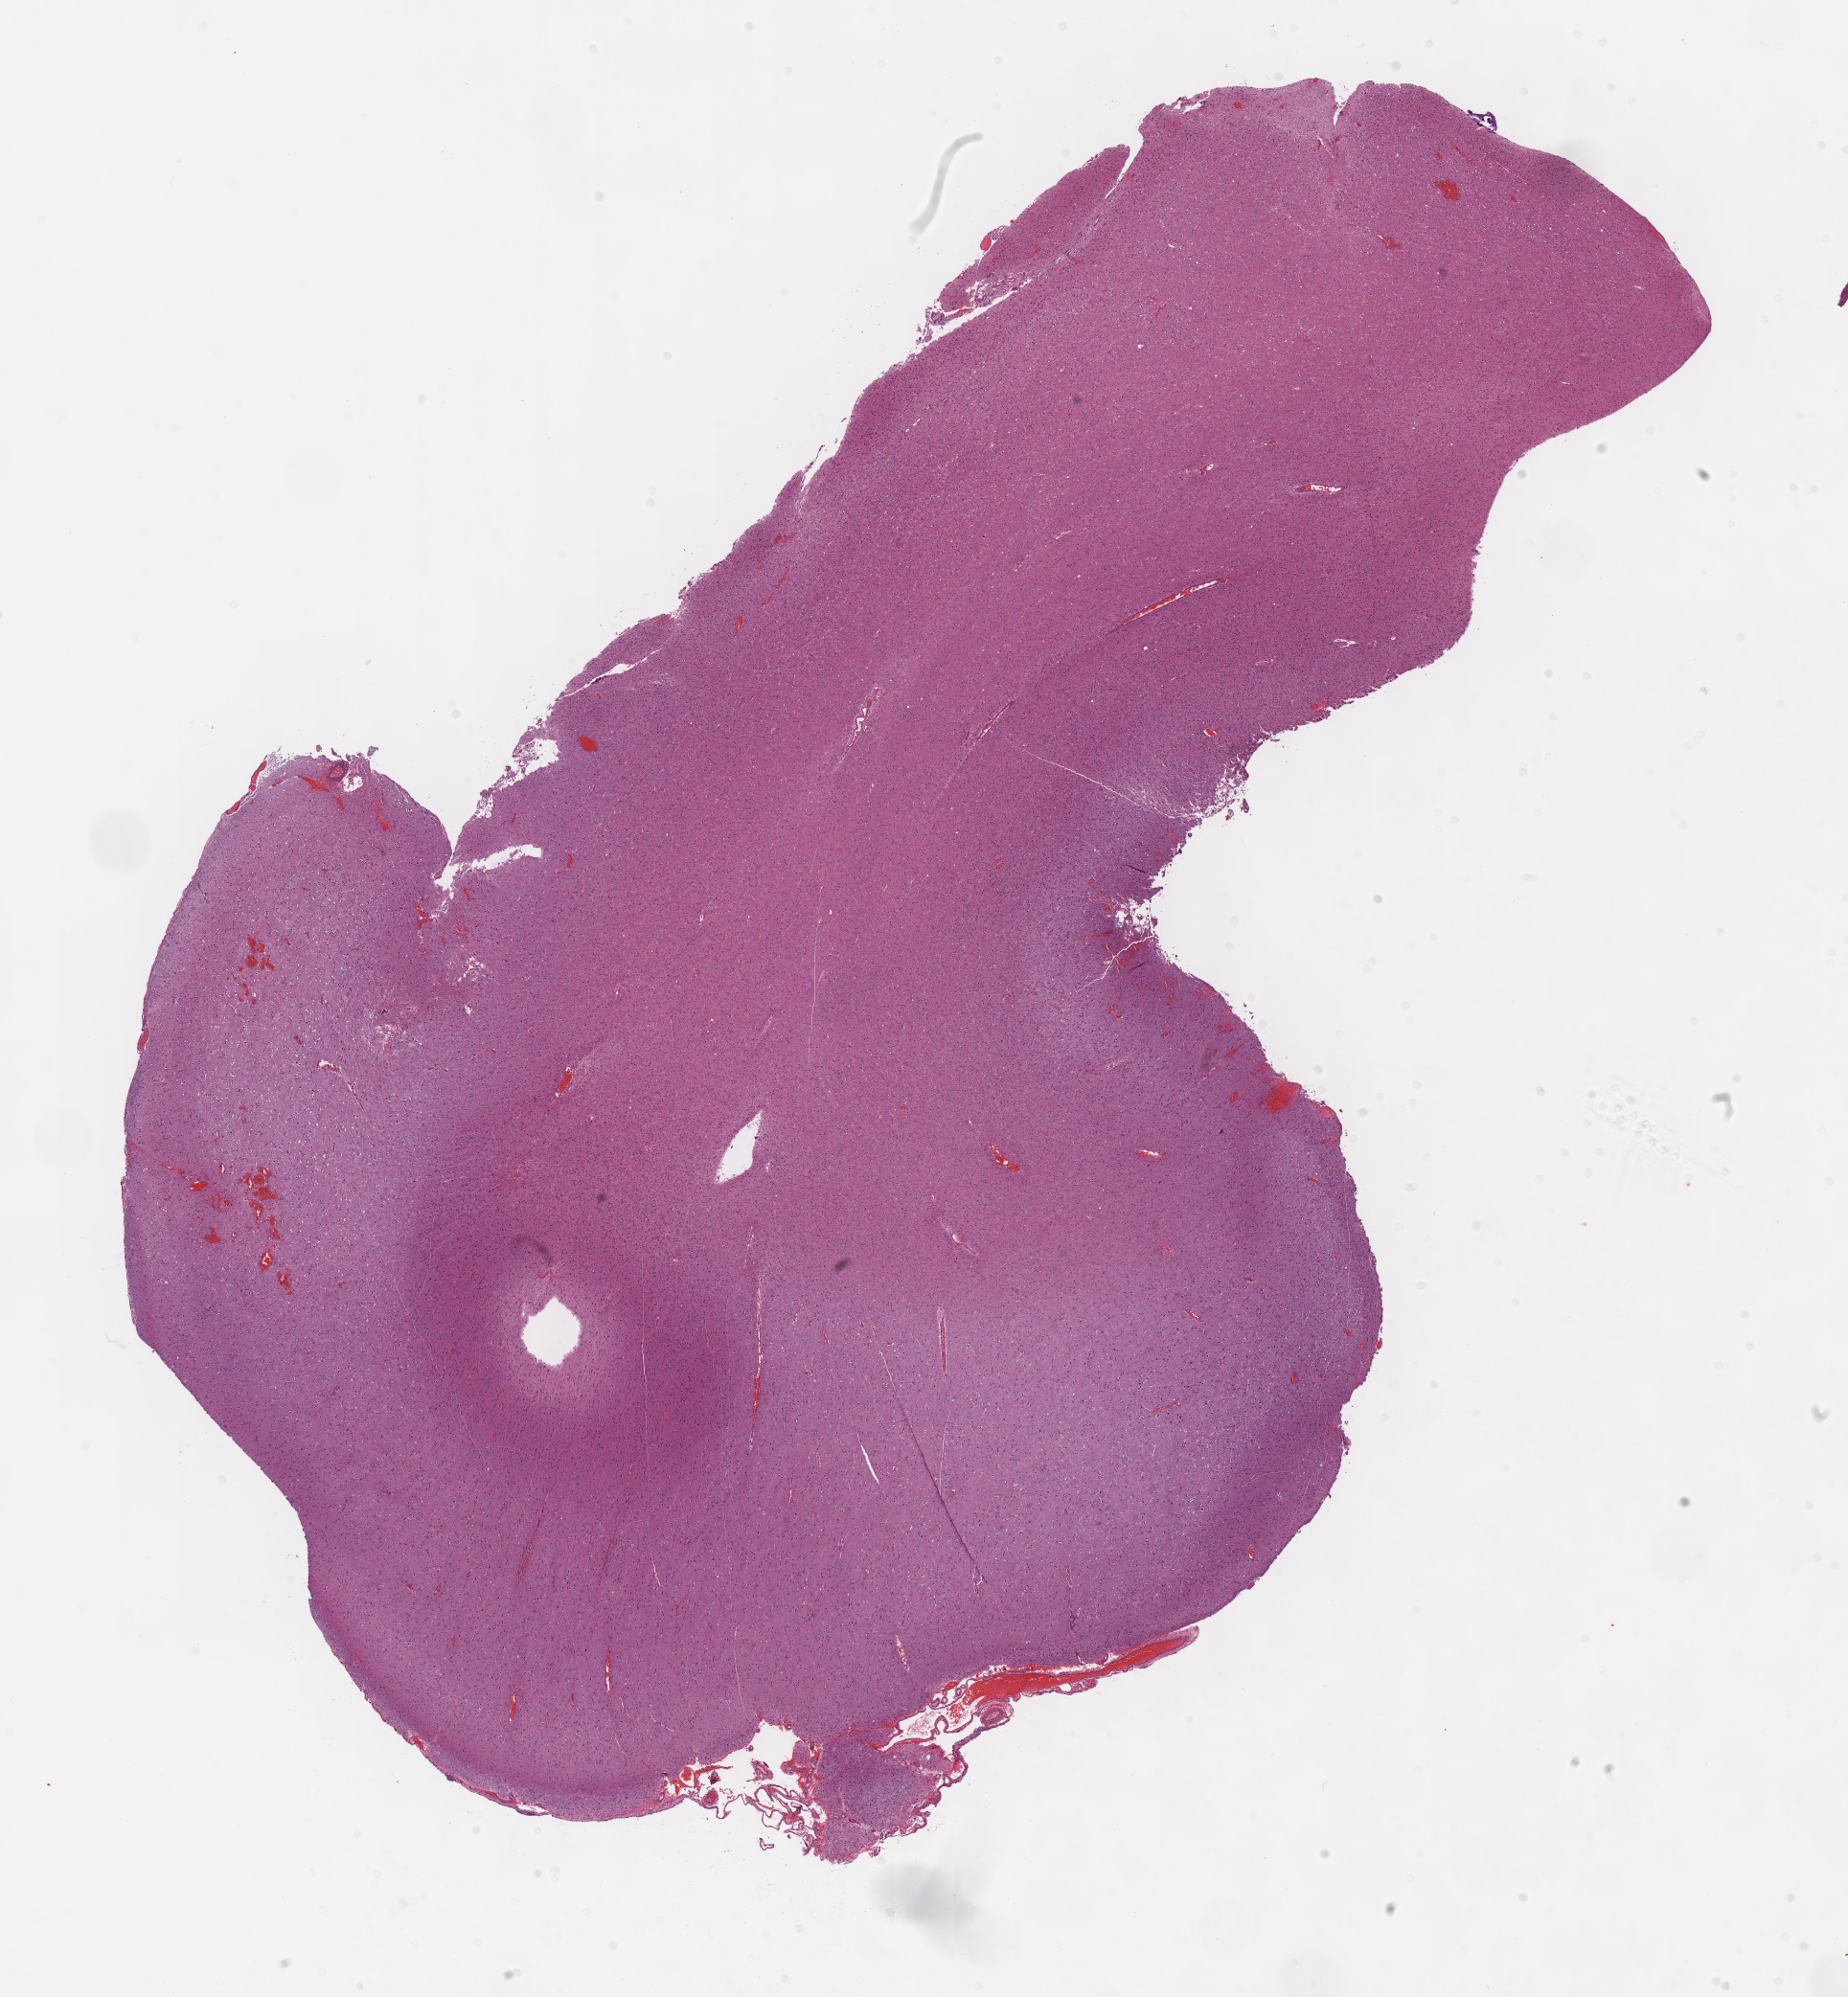
Whole-slide histology image, H&E — shown as a low-resolution overview of the whole scanned area (about 15.6 x 16.9 mm, slide scanned at 40x). Formalin-fixed paraffin-embedded (FFPE) diagnostic section. Primary tumour sample from the brain. Patient: male, age at initial diagnosis 37 years. Histologic grade: G3 (poorly differentiated).
Laterality: right. Diagnosis: Oligodendroglioma, anaplastic.